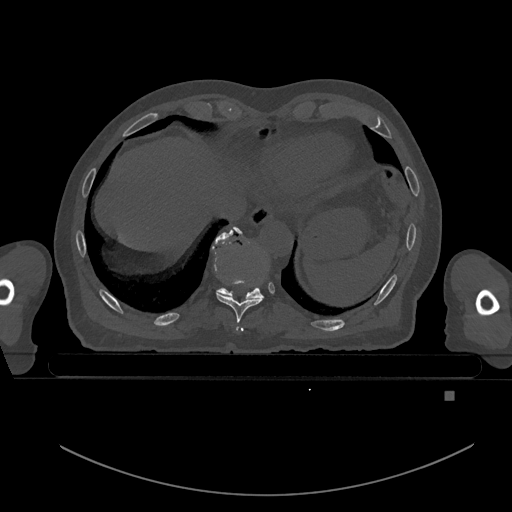
CT including the spine, one axial slice; slice 126 of 969 in the series (ordered by position); bone window (W 1800 / L 400 HU); 512 × 512 image matrix, field of view 456 × 456 mm. Male patient, age 82 years. Case-level facts recorded for this patient, not image findings: primary cancer: prostate.
Outlined on this slice (semi-automatic segmentation, software-assisted and operator-edited):
- T10 vertebra: box from (x=218, y=226) to (x=267, y=298) px
- T9 vertebra: (x=212, y=230)–(x=264, y=331)